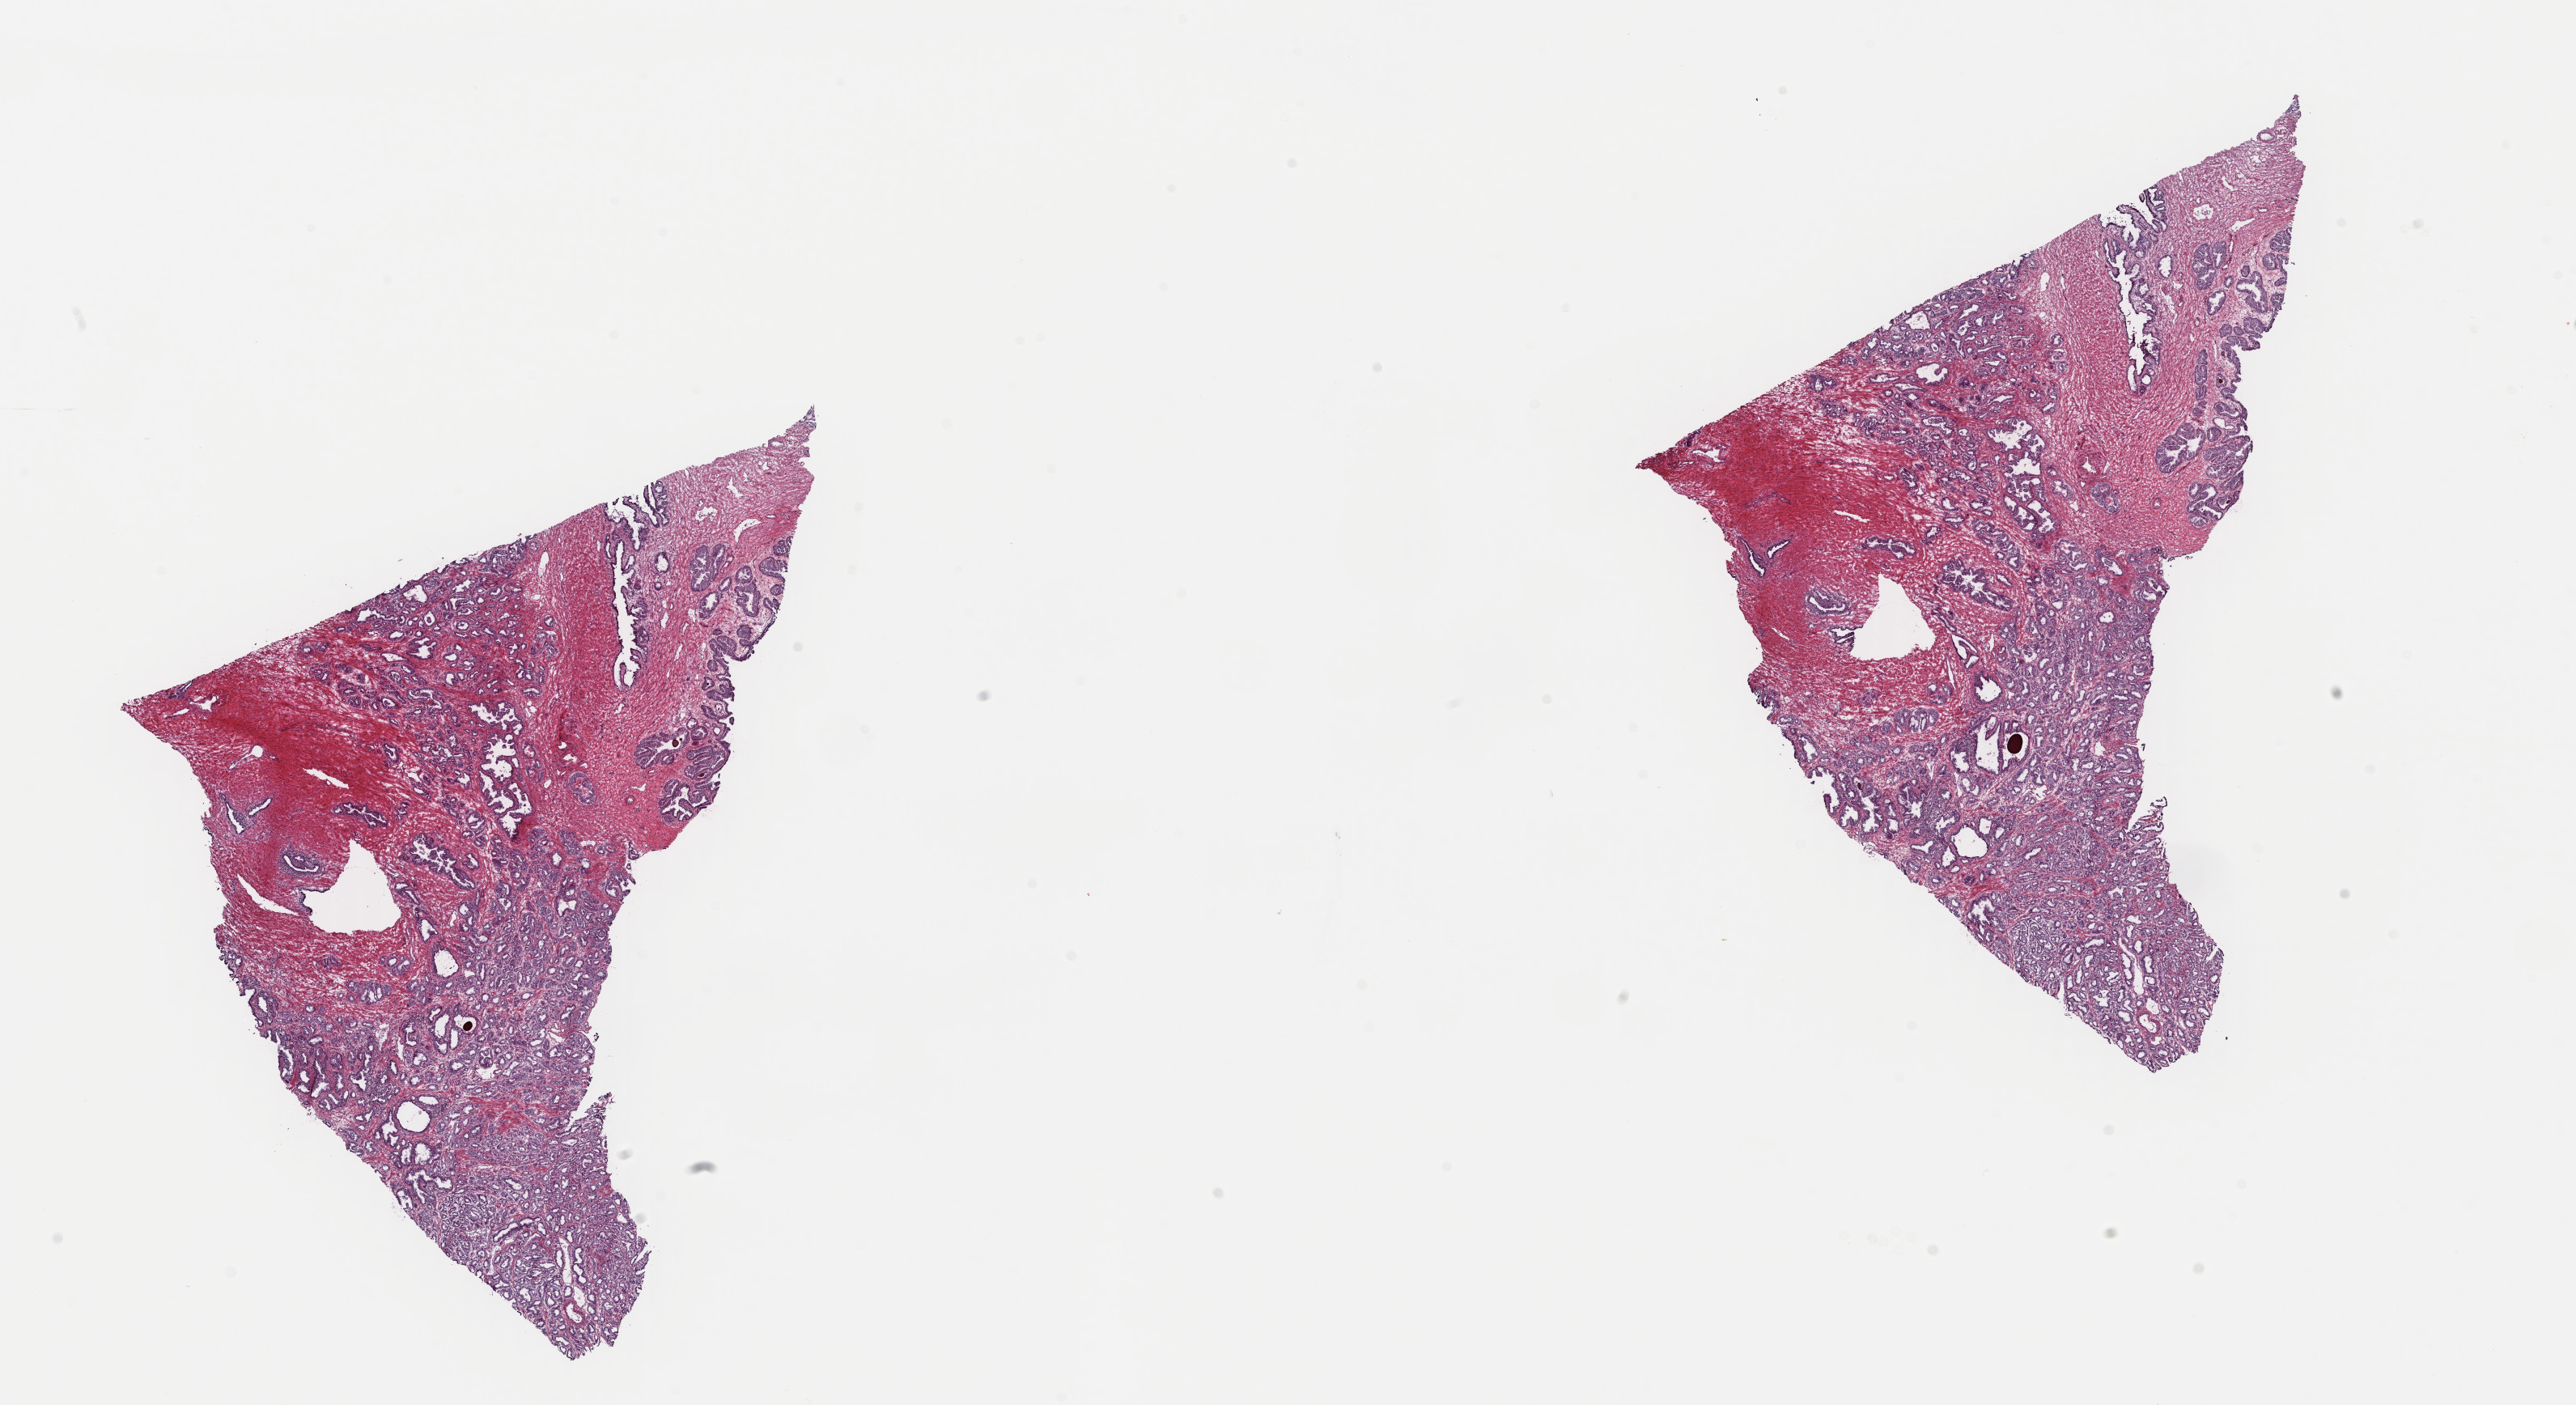
Hematoxylin and eosin (H&E) stained whole-slide image — shown as a low-resolution overview of the whole scanned area (about 25.1 x 13.7 mm, slide scanned at 40x), frozen section from the top of the tissue portion, sample: primary tumour, prostate. Male, age 67 years at initial diagnosis. Gleason score: 7 (4+3). Composition of this section per pathologist review: tumour cells 60%, tumour nuclei 80%, normal cells 25%, stromal cells 15%, necrosis 0%. Infiltration values recorded for this section: lymphocyte infiltration 1%, monocyte infiltration 1%, neutrophil infiltration 0%.
Diagnosis: Adenocarcinoma with mixed subtypes (prostate gland). Lymph nodes positive (case pathology): 0 of 23 examined.